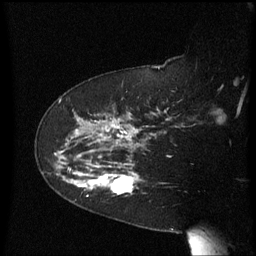
Breast MRI (dynamic contrast-enhanced), one sagittal slice; position 43 of 60 along the scan axis; dynamic contrast-enhanced series, image 2 of 3 at this slice position (ordered by acquisition); 1.5 T; TE 4.2 ms, TR 8.4 ms; 2.3 mm slice thickness; 256 × 256 image matrix, field of view 200 × 200 mm. Patient: female, 63 years. Case-level facts recorded for this patient, not image findings: setting: breast cancer imaged before/during neoadjuvant chemotherapy; receptor status: HER2-positive.
Structures marked on this image (semi-automatically segmented with operator editing):
- analysis volume of interest (the breast-tissue region the enhancement analysis was run in; not a lesion): bounding box <63,144,147,205> (left, top, right, bottom; pixels)
- tumour enhancement mask (voxels above the 70 % enhancement threshold inside the analysis volume of interest): <64,172,138,194>